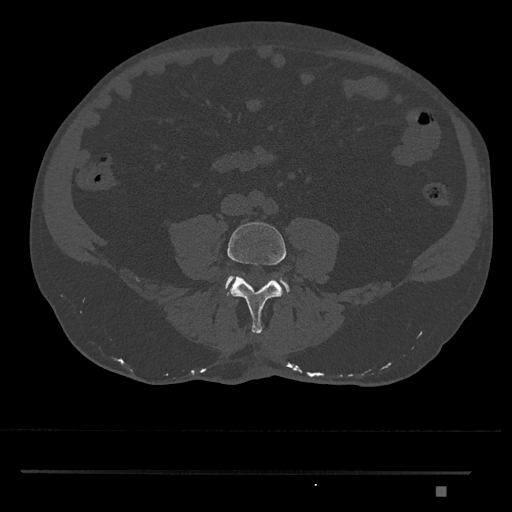
CT including the spine, one axial slice; slice 604 of 1134 in the series (ordered by position); reconstruction kernel Br40s/3; 120 kVp; bone window (W 1800 / L 400 HU); 0.5 mm slice thickness; 512 × 512 image matrix, field of view 429 × 429 mm. Patient: male, 65 years. From the clinical record (not read from this slice): primary cancer: prostate.
Structures marked on this image (semi-automatic segmentation, software-assisted and operator-edited):
- L4 vertebra: box from (x=227, y=222) to (x=286, y=334) px
- L5 vertebra: (x=225, y=277)–(x=289, y=293)